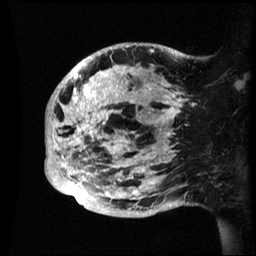
Breast MRI (dynamic contrast-enhanced), one sagittal slice; slice 18 of 60 in the series (ordered by position); dynamic contrast-enhanced series, image 2 of 3 at this slice position (ordered by acquisition); 1.5 T; TE 4.2 ms, TR 8.4 ms; 2.4 mm slice thickness; 256 × 256 image matrix. Patient: female, 48 years.
Structures marked on this image (semi-automatic segmentation, software-assisted and operator-edited):
- analysis volume of interest (the breast-tissue region the enhancement analysis was run in; not a lesion): bounding box <45,43,190,217> (left, top, right, bottom; pixels)
- tumour enhancement mask (voxels above the 70 % enhancement threshold inside the analysis volume of interest): <46,43,181,201>